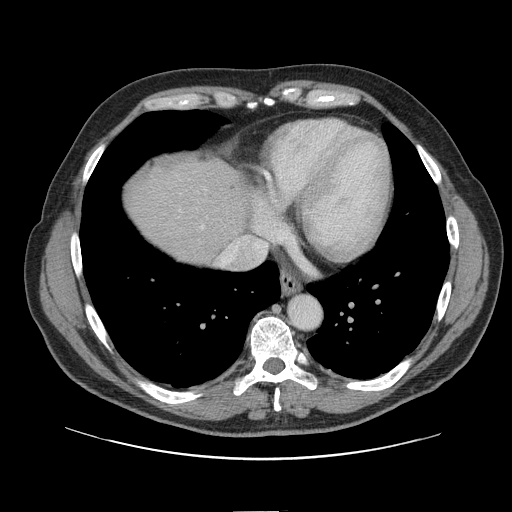
Contrast-enhanced abdominal CT, one axial slice. Soft-tissue window (W 400 / L 40 HU). 512 × 512 image matrix, field of view 412 × 412 mm. Male patient, age 66 years. Case-level facts recorded for this patient, not image findings: diagnosis: colorectal cancer liver metastases, imaged before liver resection; multiple liver metastases: no; largest metastasis: 3.5 cm; disease in both lobes: no.
Outlined on this slice (manually delineated by an expert):
- hepatic veins: bounding box [x1, y1, x2, y2] px = [202, 226, 241, 267]
- liver: [129, 163, 246, 263]
- planned liver remnant (the part of the liver to remain after resection): [129, 163, 246, 264]
- liver metastasis: [232, 185, 237, 190]